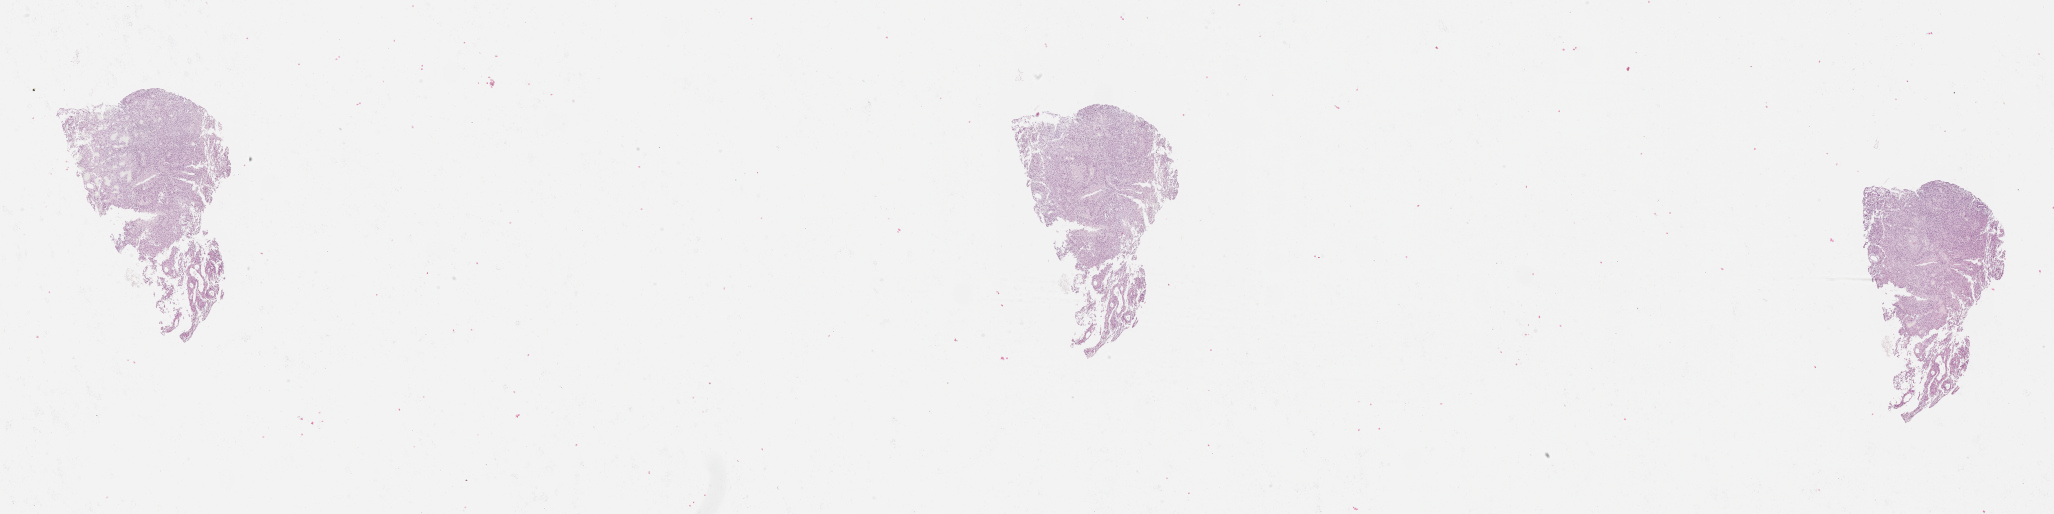
Digitized H&E-stained tissue section (whole slide), whole scanned area (about 33.1 x 8.3 mm, from a 20x scan) shown as a low-resolution overview; tumour tissue sample, sampled site: brain. 63-year-old female patient. Slide review estimates, as recorded: tumour nuclei 75%, necrosis 5%.
• primary tumour site (as recorded): temporal lobe
• diagnosis: Glioblastoma